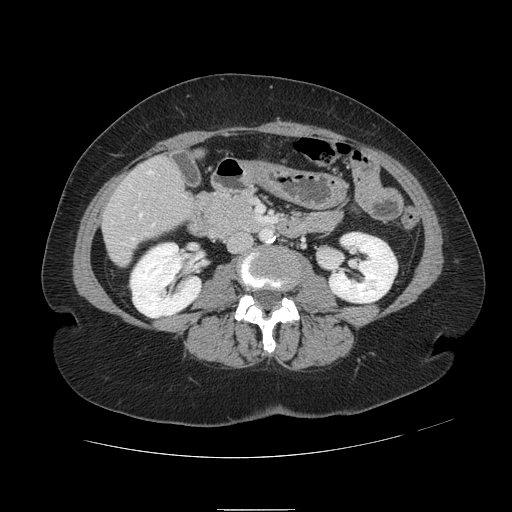
Contrast-enhanced abdominal CT, one axial slice; slice 24 of 121 in the series (ordered by position); 120 kVp; intravenous contrast given; soft-tissue window (W 400 / L 40 HU); 2.5 mm slice thickness; 512 × 512 image matrix, field of view 400 × 400 mm. Female patient, age 52 years. Case-level facts recorded for this patient, not image findings: diagnosis: colorectal cancer liver metastases, imaged before liver resection; multiple liver metastases: yes; largest metastasis: 6.3 cm; disease in both lobes: no.
Structures marked on this image (outlined manually by an expert reader):
- hepatic veins: bounding box <132,171,155,240> (left, top, right, bottom; pixels)
- liver: <104,158,189,265>